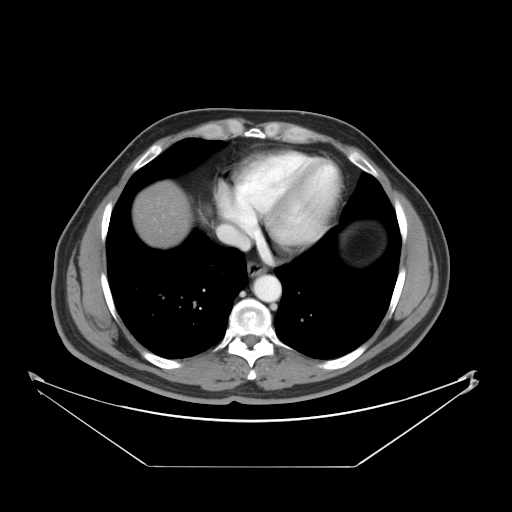
Contrast-enhanced abdominal CT, one axial slice. Slice 42 of 46 in the series (ordered by position). Reconstruction kernel STANDARD. 120 kVp. Intravenous contrast given. Soft-tissue window (W 400 / L 40 HU). 512 × 512 image matrix. Male patient, age 57 years. From the clinical record (not read from this slice): diagnosis: colorectal cancer liver metastases, imaged before liver resection; multiple liver metastases: no; largest metastasis: 3.3 cm.
Annotated regions visible in this slice (outlined manually by an expert reader):
- liver: bounding box [x1, y1, x2, y2] px = [134, 185, 191, 246]
- planned liver remnant (the part of the liver to remain after resection): [134, 185, 191, 245]